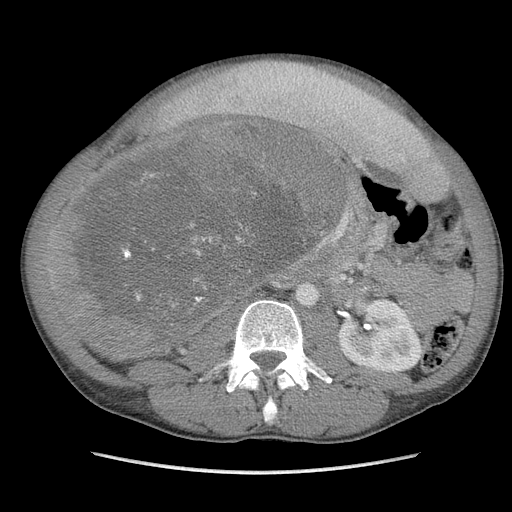
Contrast-enhanced abdominal CT, one axial slice; position 51 of 115 along the scan axis; soft-tissue window (W 400 / L 40 HU); 5 mm slice thickness; 512 × 512 image matrix, field of view 360 × 360 mm. Male patient. Case-level facts recorded for this patient, not image findings: diagnosis: adrenocortical carcinoma; tumour side: right adrenal; Ki-67 index: 13 %; stage (as recorded): 3.
Annotated regions visible in this slice (semi-automatically segmented with operator editing):
- mass: box from (x=66, y=121) to (x=337, y=357) px